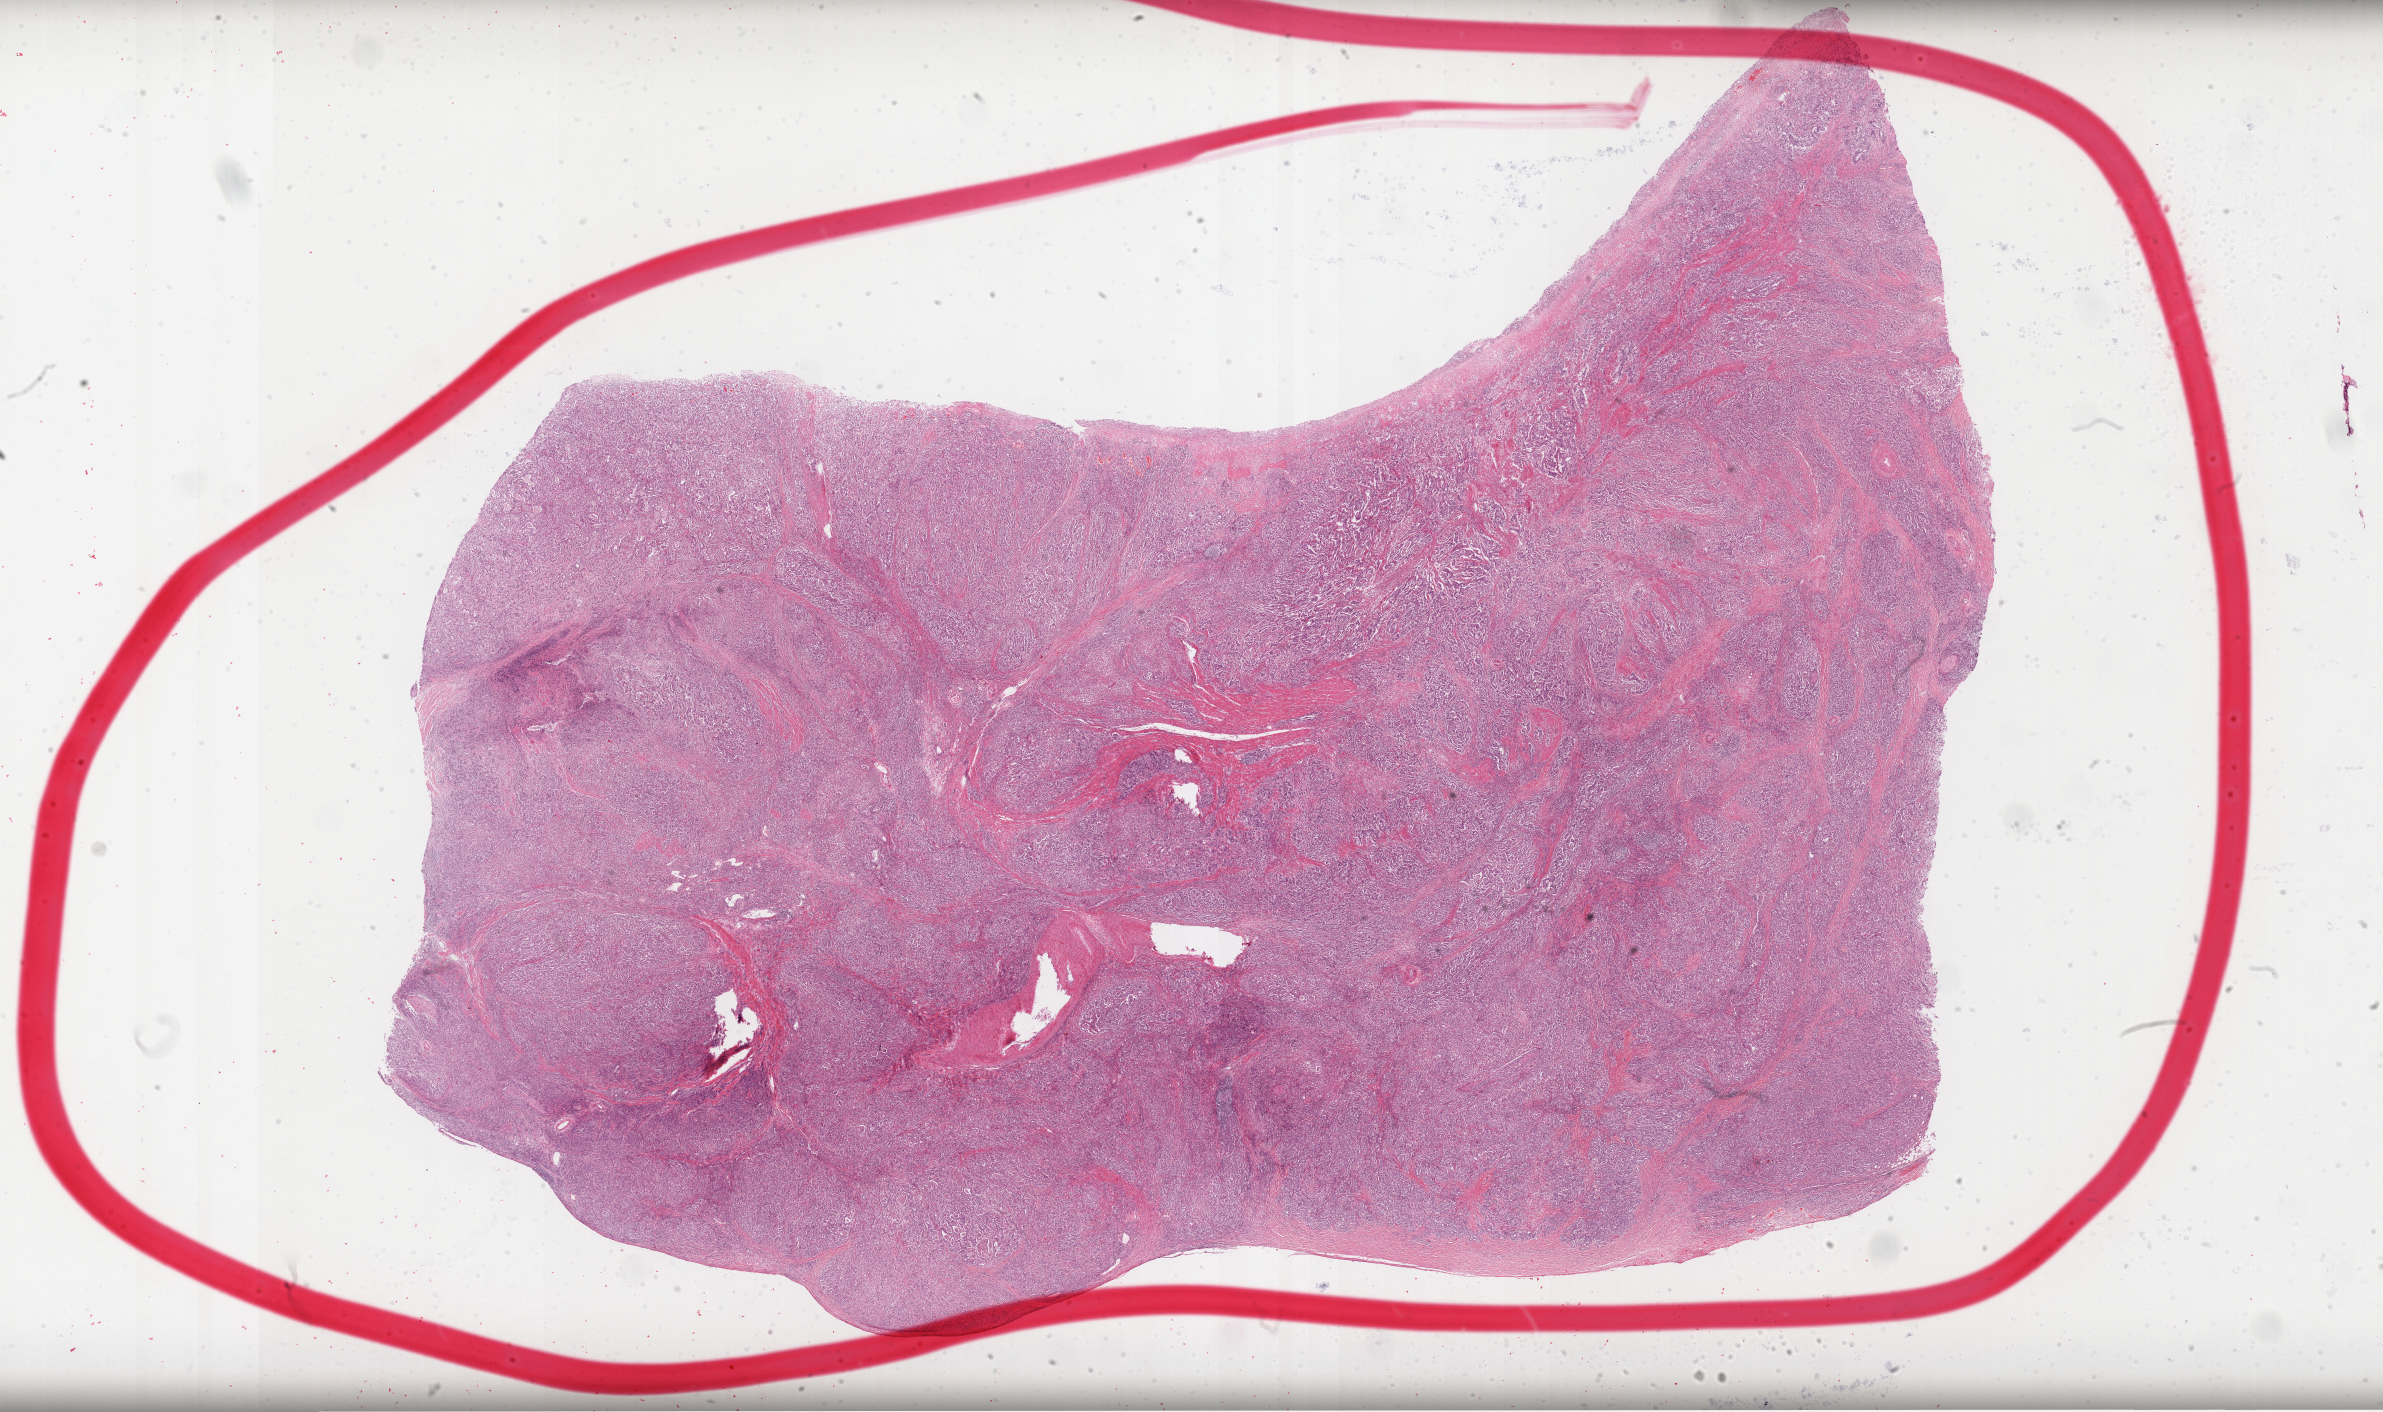
Whole-slide histology image, H&E-stained, whole scanned area (about 38.4 x 22.8 mm, acquisition: 40x scan) shown as a low-resolution overview, formalin-fixed paraffin-embedded (FFPE) diagnostic section, stomach, primary tumour sample. Female patient; age at initial diagnosis 57 years. Histologic grade: G3 (poorly differentiated).
• histologic diagnosis: Adenocarcinoma, intestinal type (gastric antrum)
• AJCC pathologic stage: IIIC (7th edition)